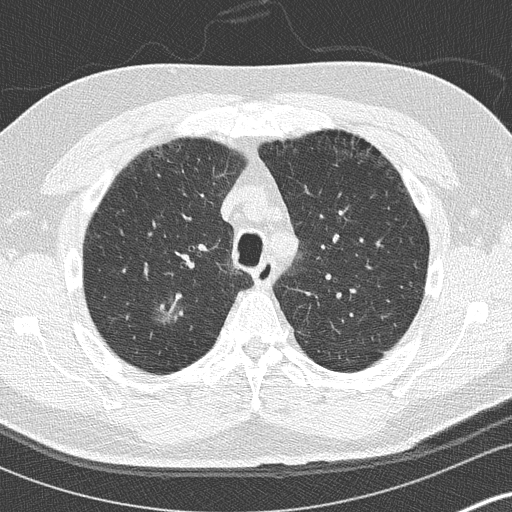
Axial slice from a low-dose chest CT screening exam; baseline screening round; lung window (W 1500 / L -600 HU); 2 mm slice thickness; lung (sharp) reconstruction kernel (B50f); 120 kVp; slice 38 of 136 in the series. Male participant, aged 59 years at enrolment. Current smoker at enrolment.
Lesion marked by an expert reader, bounding box <146,288,201,343> (left, top, right, bottom; pixels). Screening reader's record for this exam (one nodule recorded; not confirmed to be the boxed lesion): non-calcified nodule or mass ≥4 mm, right upper lobe, 16 × 16 mm, ground glass attenuation.